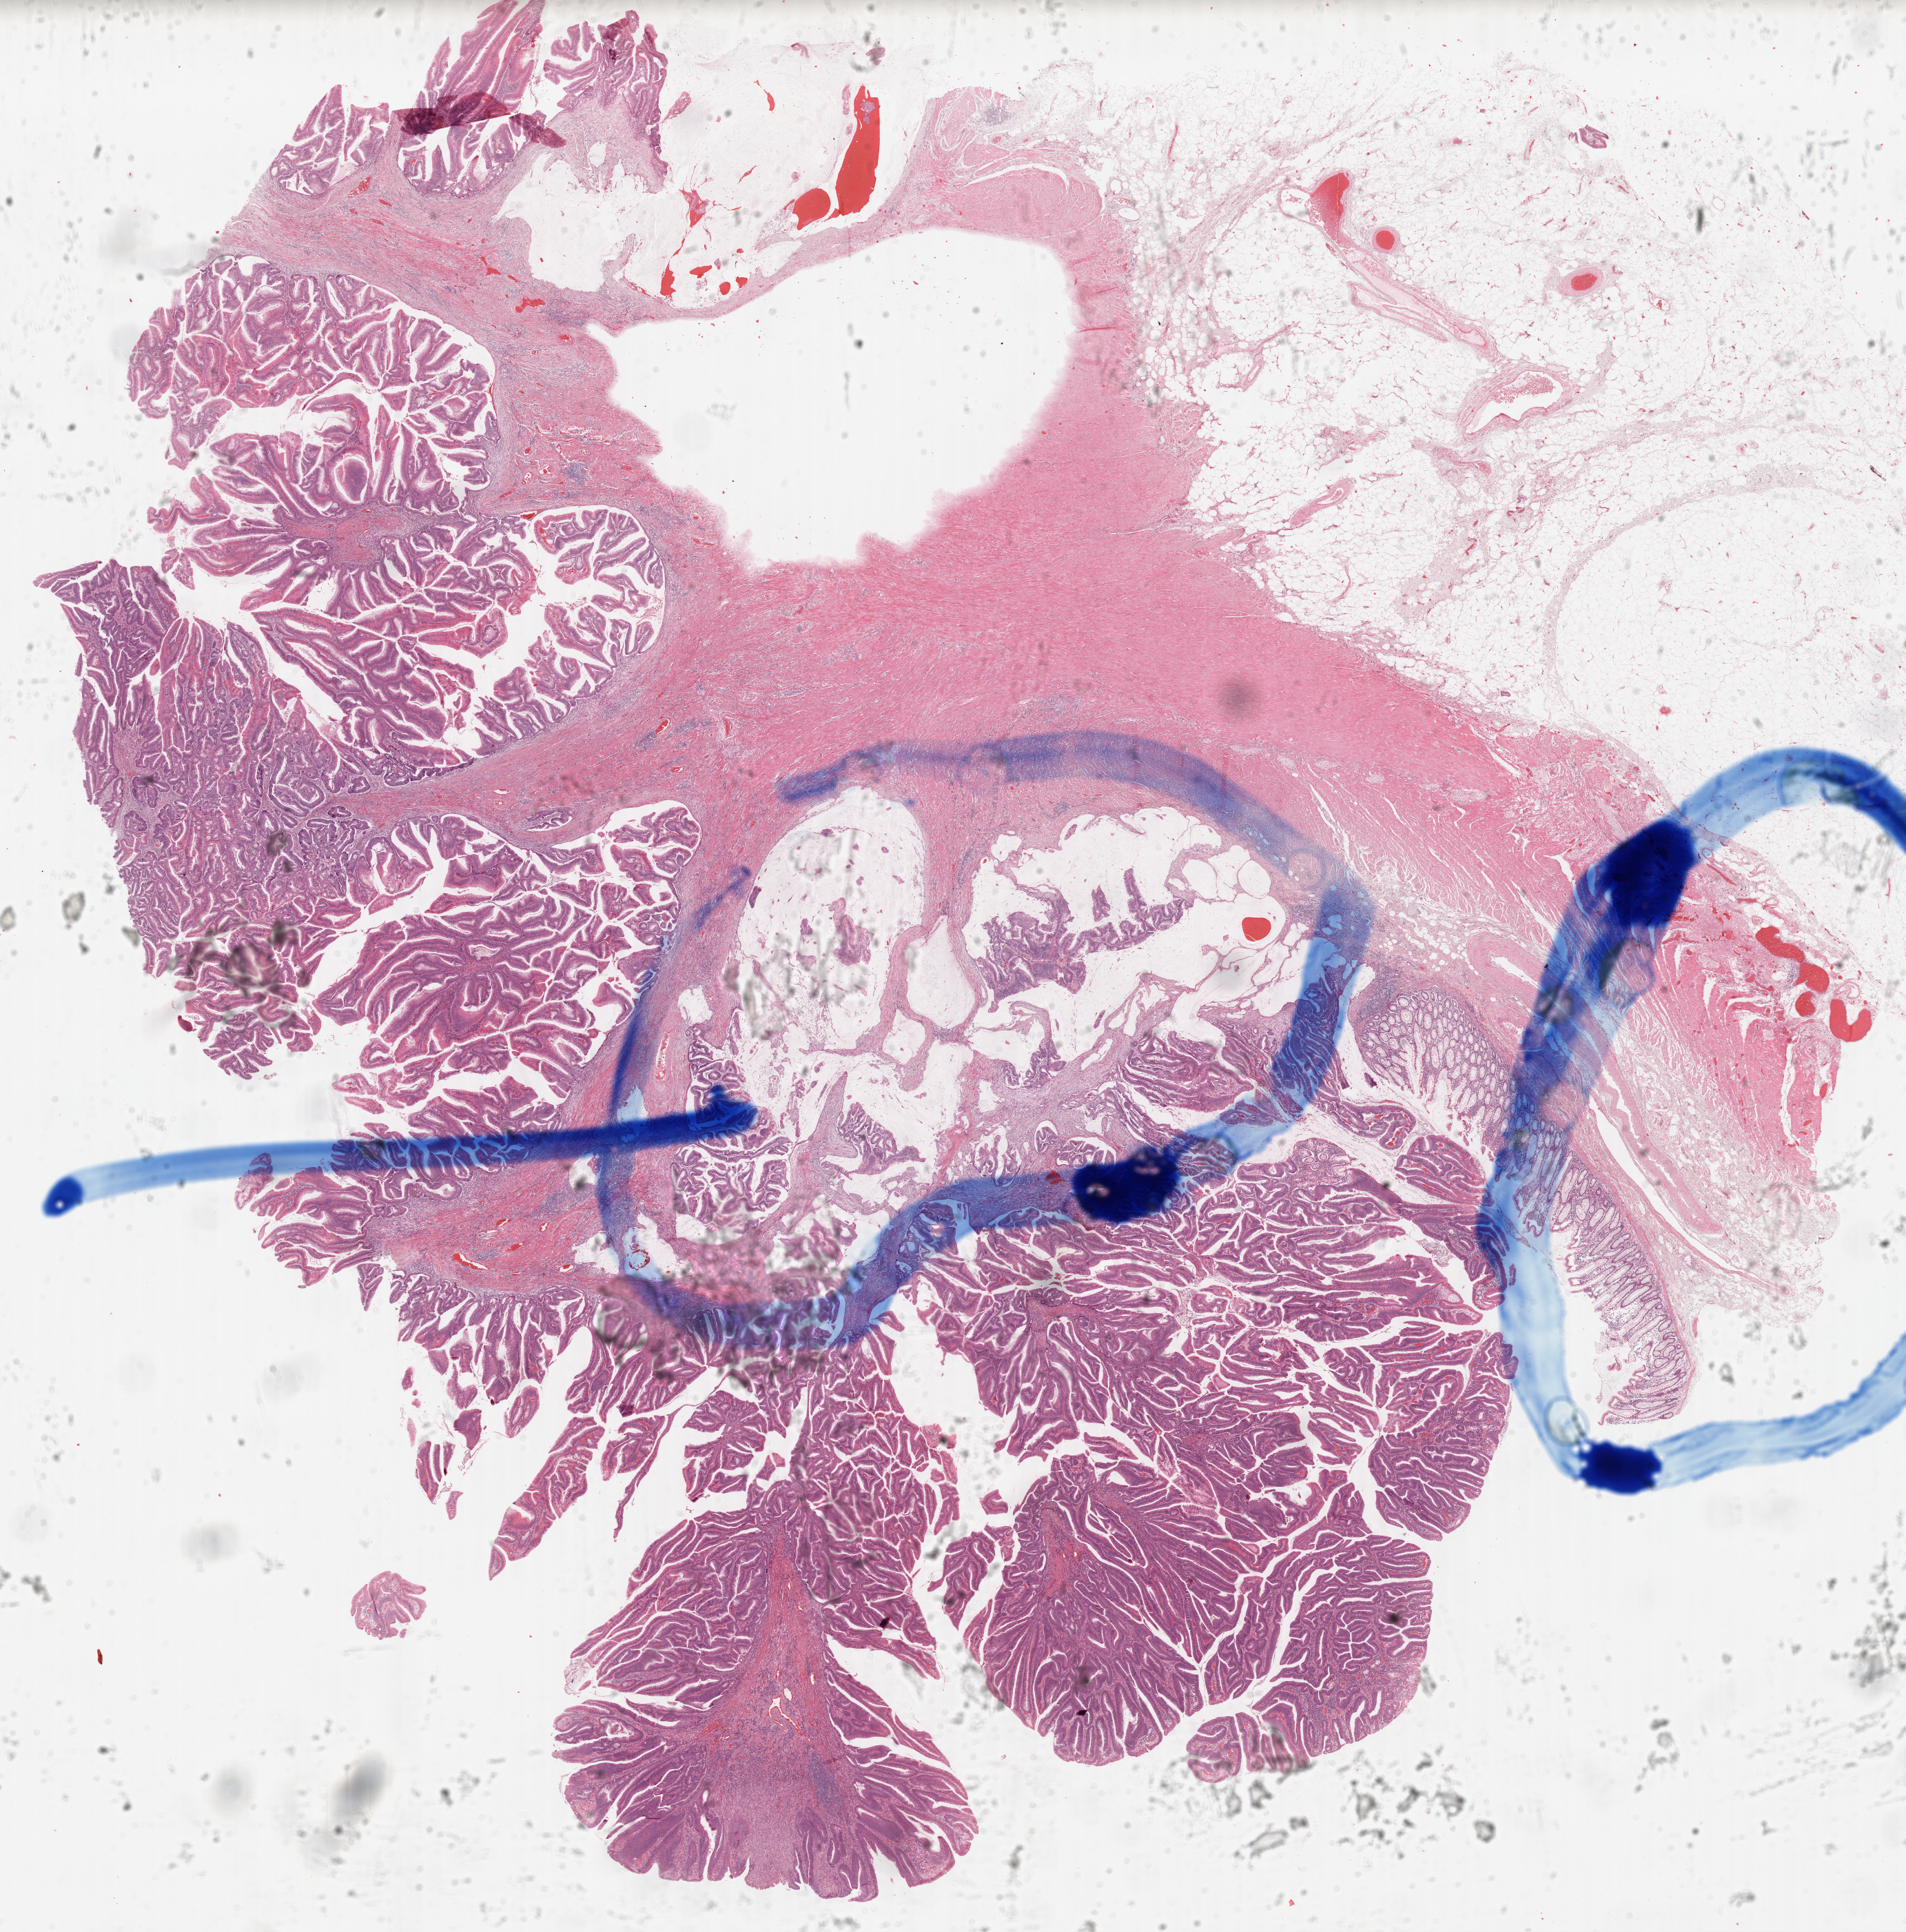
Digitized H&E tissue section (whole slide), shown as a low-resolution overview of the whole scanned area (about 21.9 x 22.1 mm, from a 40x scan); FFPE section; colon, primary tumour sample. Male patient; age at initial diagnosis 75 years.
Lymph nodes positive (case pathology): 0 of 25 examined. Pathologic diagnosis: Adenocarcinoma, NOS. AJCC pathologic stage: IIA (6th edition).